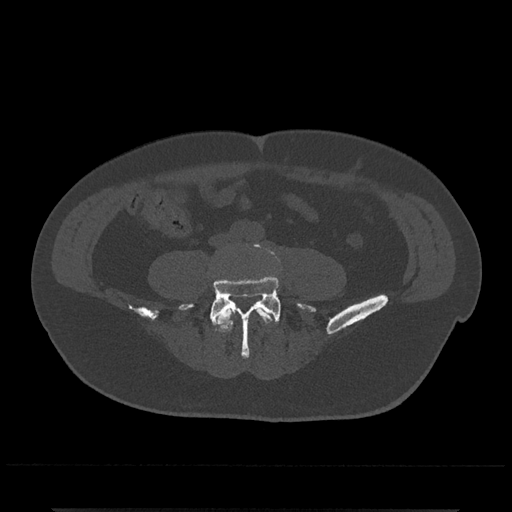
CT including the spine, one axial slice. Position 108 of 797 along the scan axis. 120 kVp. Bone window (W 1800 / L 400 HU). 512 × 512 image matrix, field of view 393 × 393 mm. Patient: male, 67 years. From the clinical record (not read from this slice): primary cancer: prostate.
Annotated regions visible in this slice (semi-automatically segmented with operator editing):
- L4 vertebra: bounding box (x1, y1, x2, y2) in pixels: (216, 302, 278, 332)
- L5 vertebra: (179, 244, 315, 358)